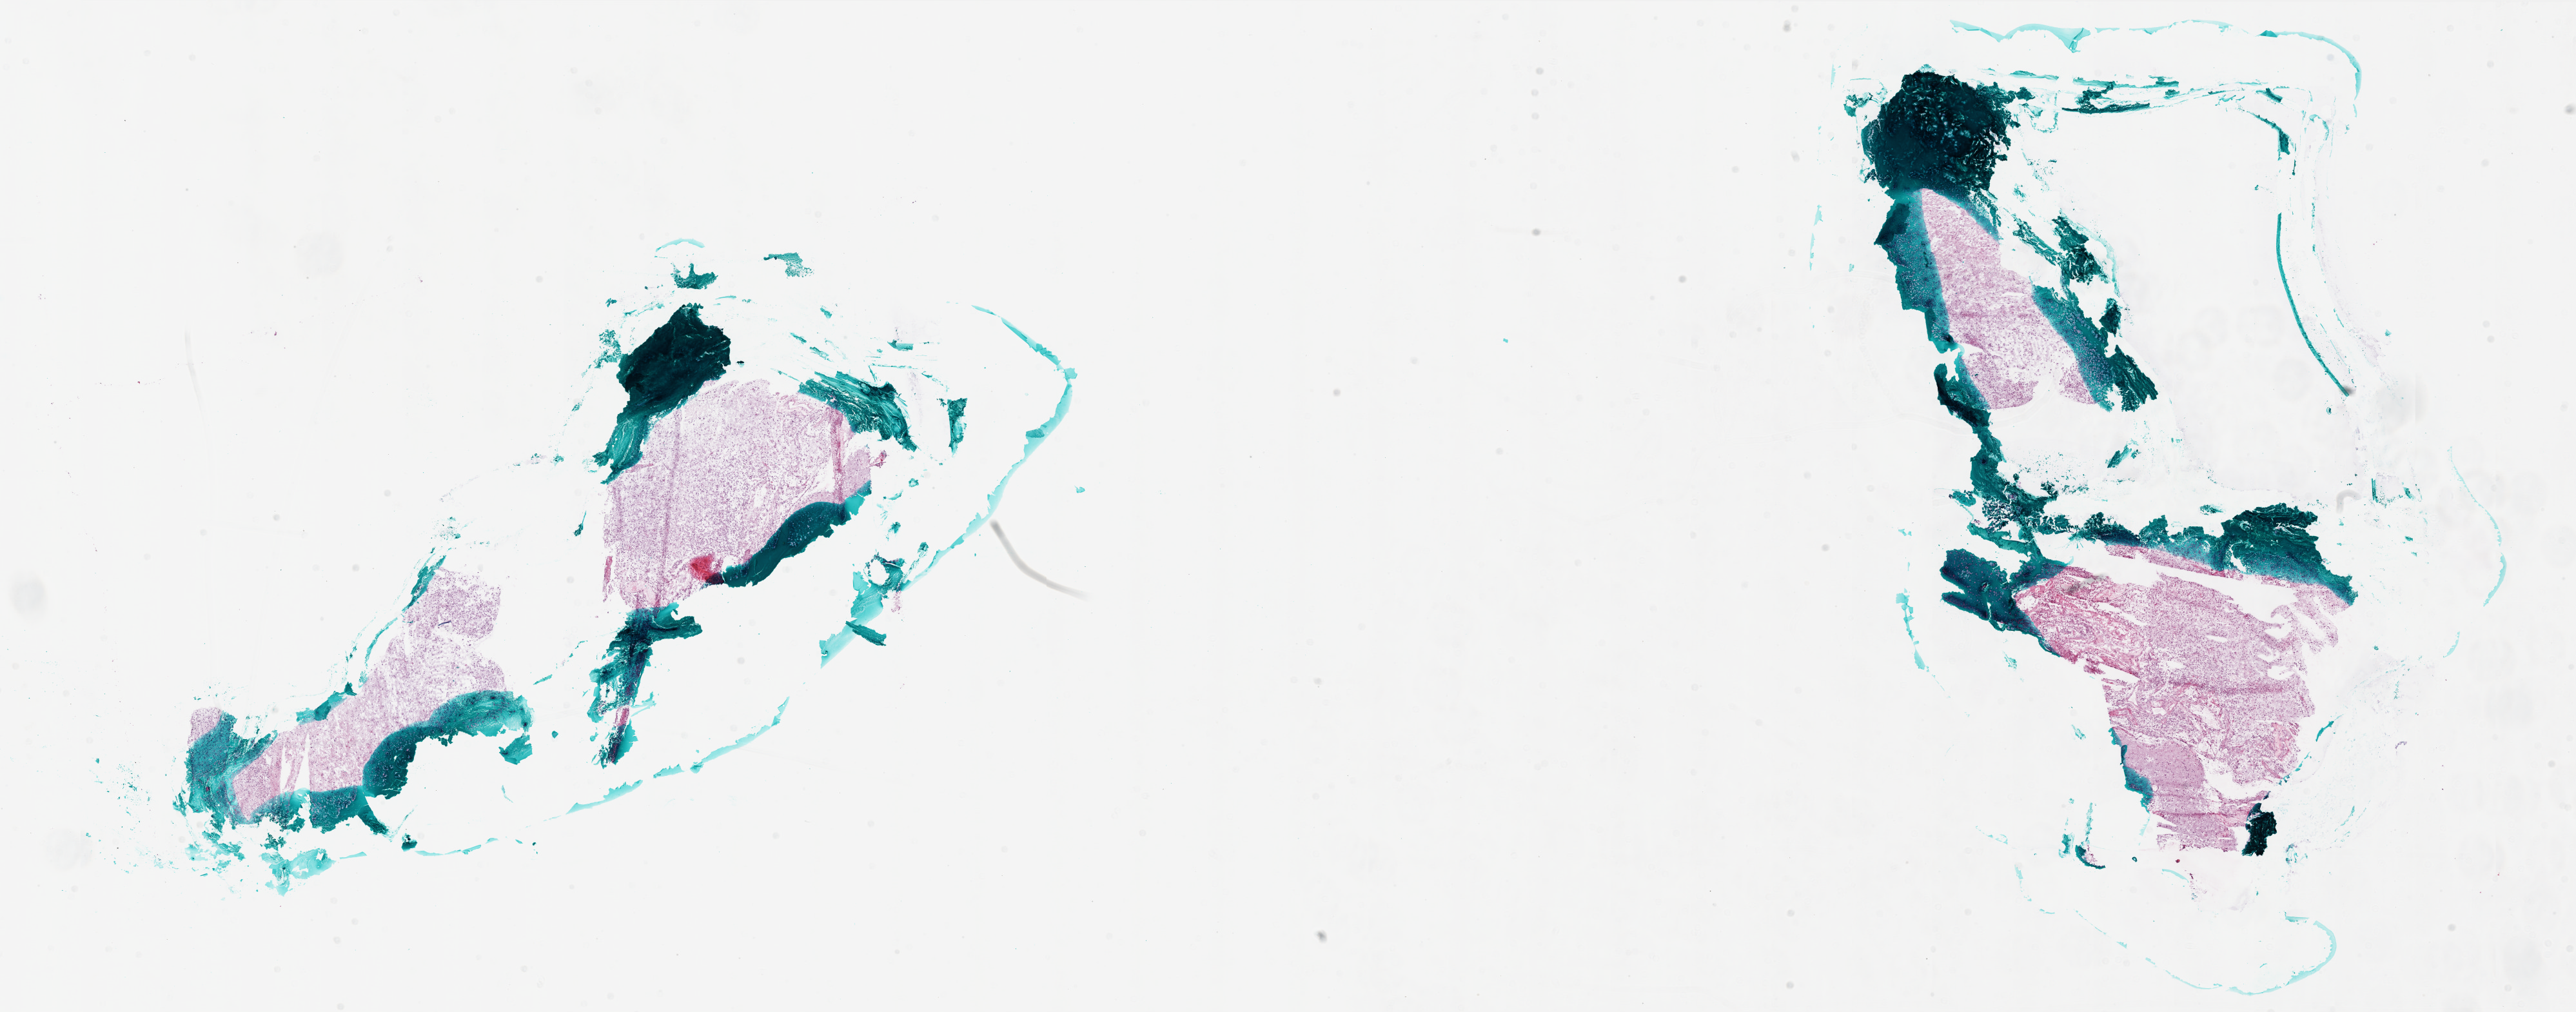
H&E whole-slide image, whole scanned area (about 32.0 x 12.6 mm, slide scanned at 20x) shown as a low-resolution overview; frozen section from the bottom of the tissue portion; primary tumour sample from the brain. Male, age 35 years at initial diagnosis. Slide review estimates, as recorded: tumour cells 50%, tumour nuclei 80%, normal cells 0%, stromal cells 40%, necrosis 10%.
• pathologic diagnosis: Glioblastoma